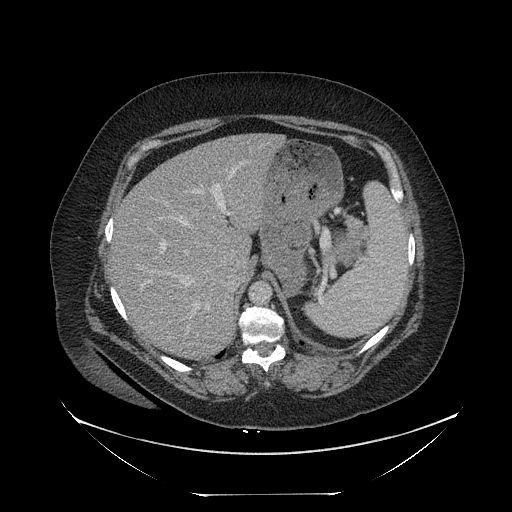
Contrast-enhanced abdominal CT, one axial slice; slice 167 of 205 in the series (ordered by position); 120 kVp; intravenous contrast given; soft-tissue window (W 400 / L 40 HU); 2.5 mm slice thickness; 512 × 512 image matrix, field of view 500 × 500 mm. Female patient, age 53 years. From the clinical record (not read from this slice): diagnosis: adrenocortical carcinoma; tumour side: left adrenal.
Structures marked on this image (semi-automatically segmented with operator editing):
- mass: bounding box (x1, y1, x2, y2) in pixels: (337, 238, 353, 261)